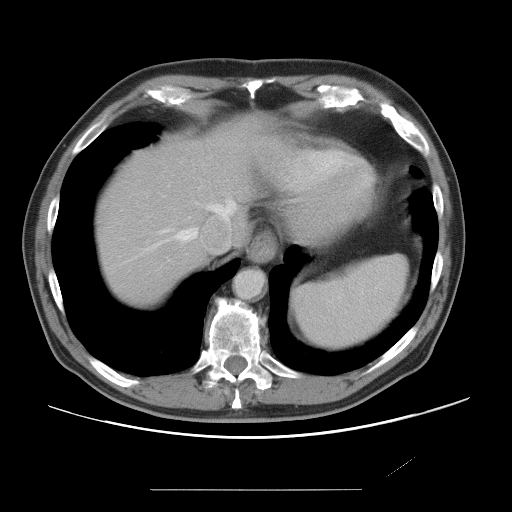
Contrast-enhanced abdominal CT, one axial slice; slice 64 of 87 in the series (ordered by position); intravenous contrast given; soft-tissue window (W 400 / L 40 HU); 5 mm slice thickness; 512 × 512 image matrix, field of view 406 × 406 mm. Male patient, age 74 years. From the clinical record (not read from this slice): diagnosis: colorectal cancer liver metastases, imaged before liver resection; multiple liver metastases: yes; largest metastasis: 1.1 cm; disease in both lobes: no.
Structures marked on this image (outlined manually by an expert reader):
- hepatic veins: bounding box <145,201,236,251> (left, top, right, bottom; pixels)
- liver: <95,124,264,301>
- planned liver remnant (the part of the liver to remain after resection): <95,123,270,301>